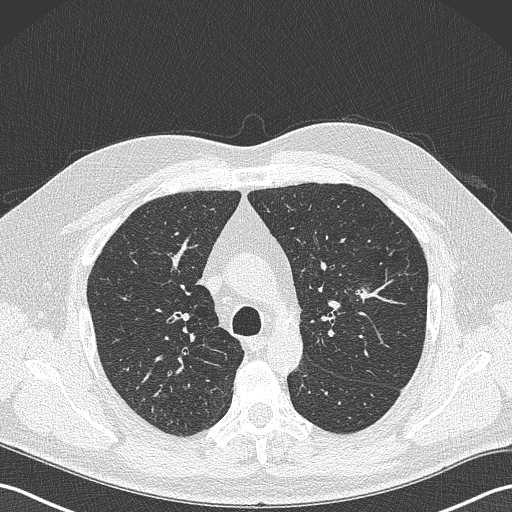
Low-dose screening chest CT, one axial slice; position 240 of 343 along the scan axis; reconstruction kernel B50f; lung window (W 1500 / L -600 HU); 1 mm slice thickness; 512 × 512 image matrix.
Outlined on this slice (expert manual segmentation):
- lesion 1 (tumor, upper lobe of left lung): bounding box (x1, y1, x2, y2) in pixels: (355, 287, 370, 302)